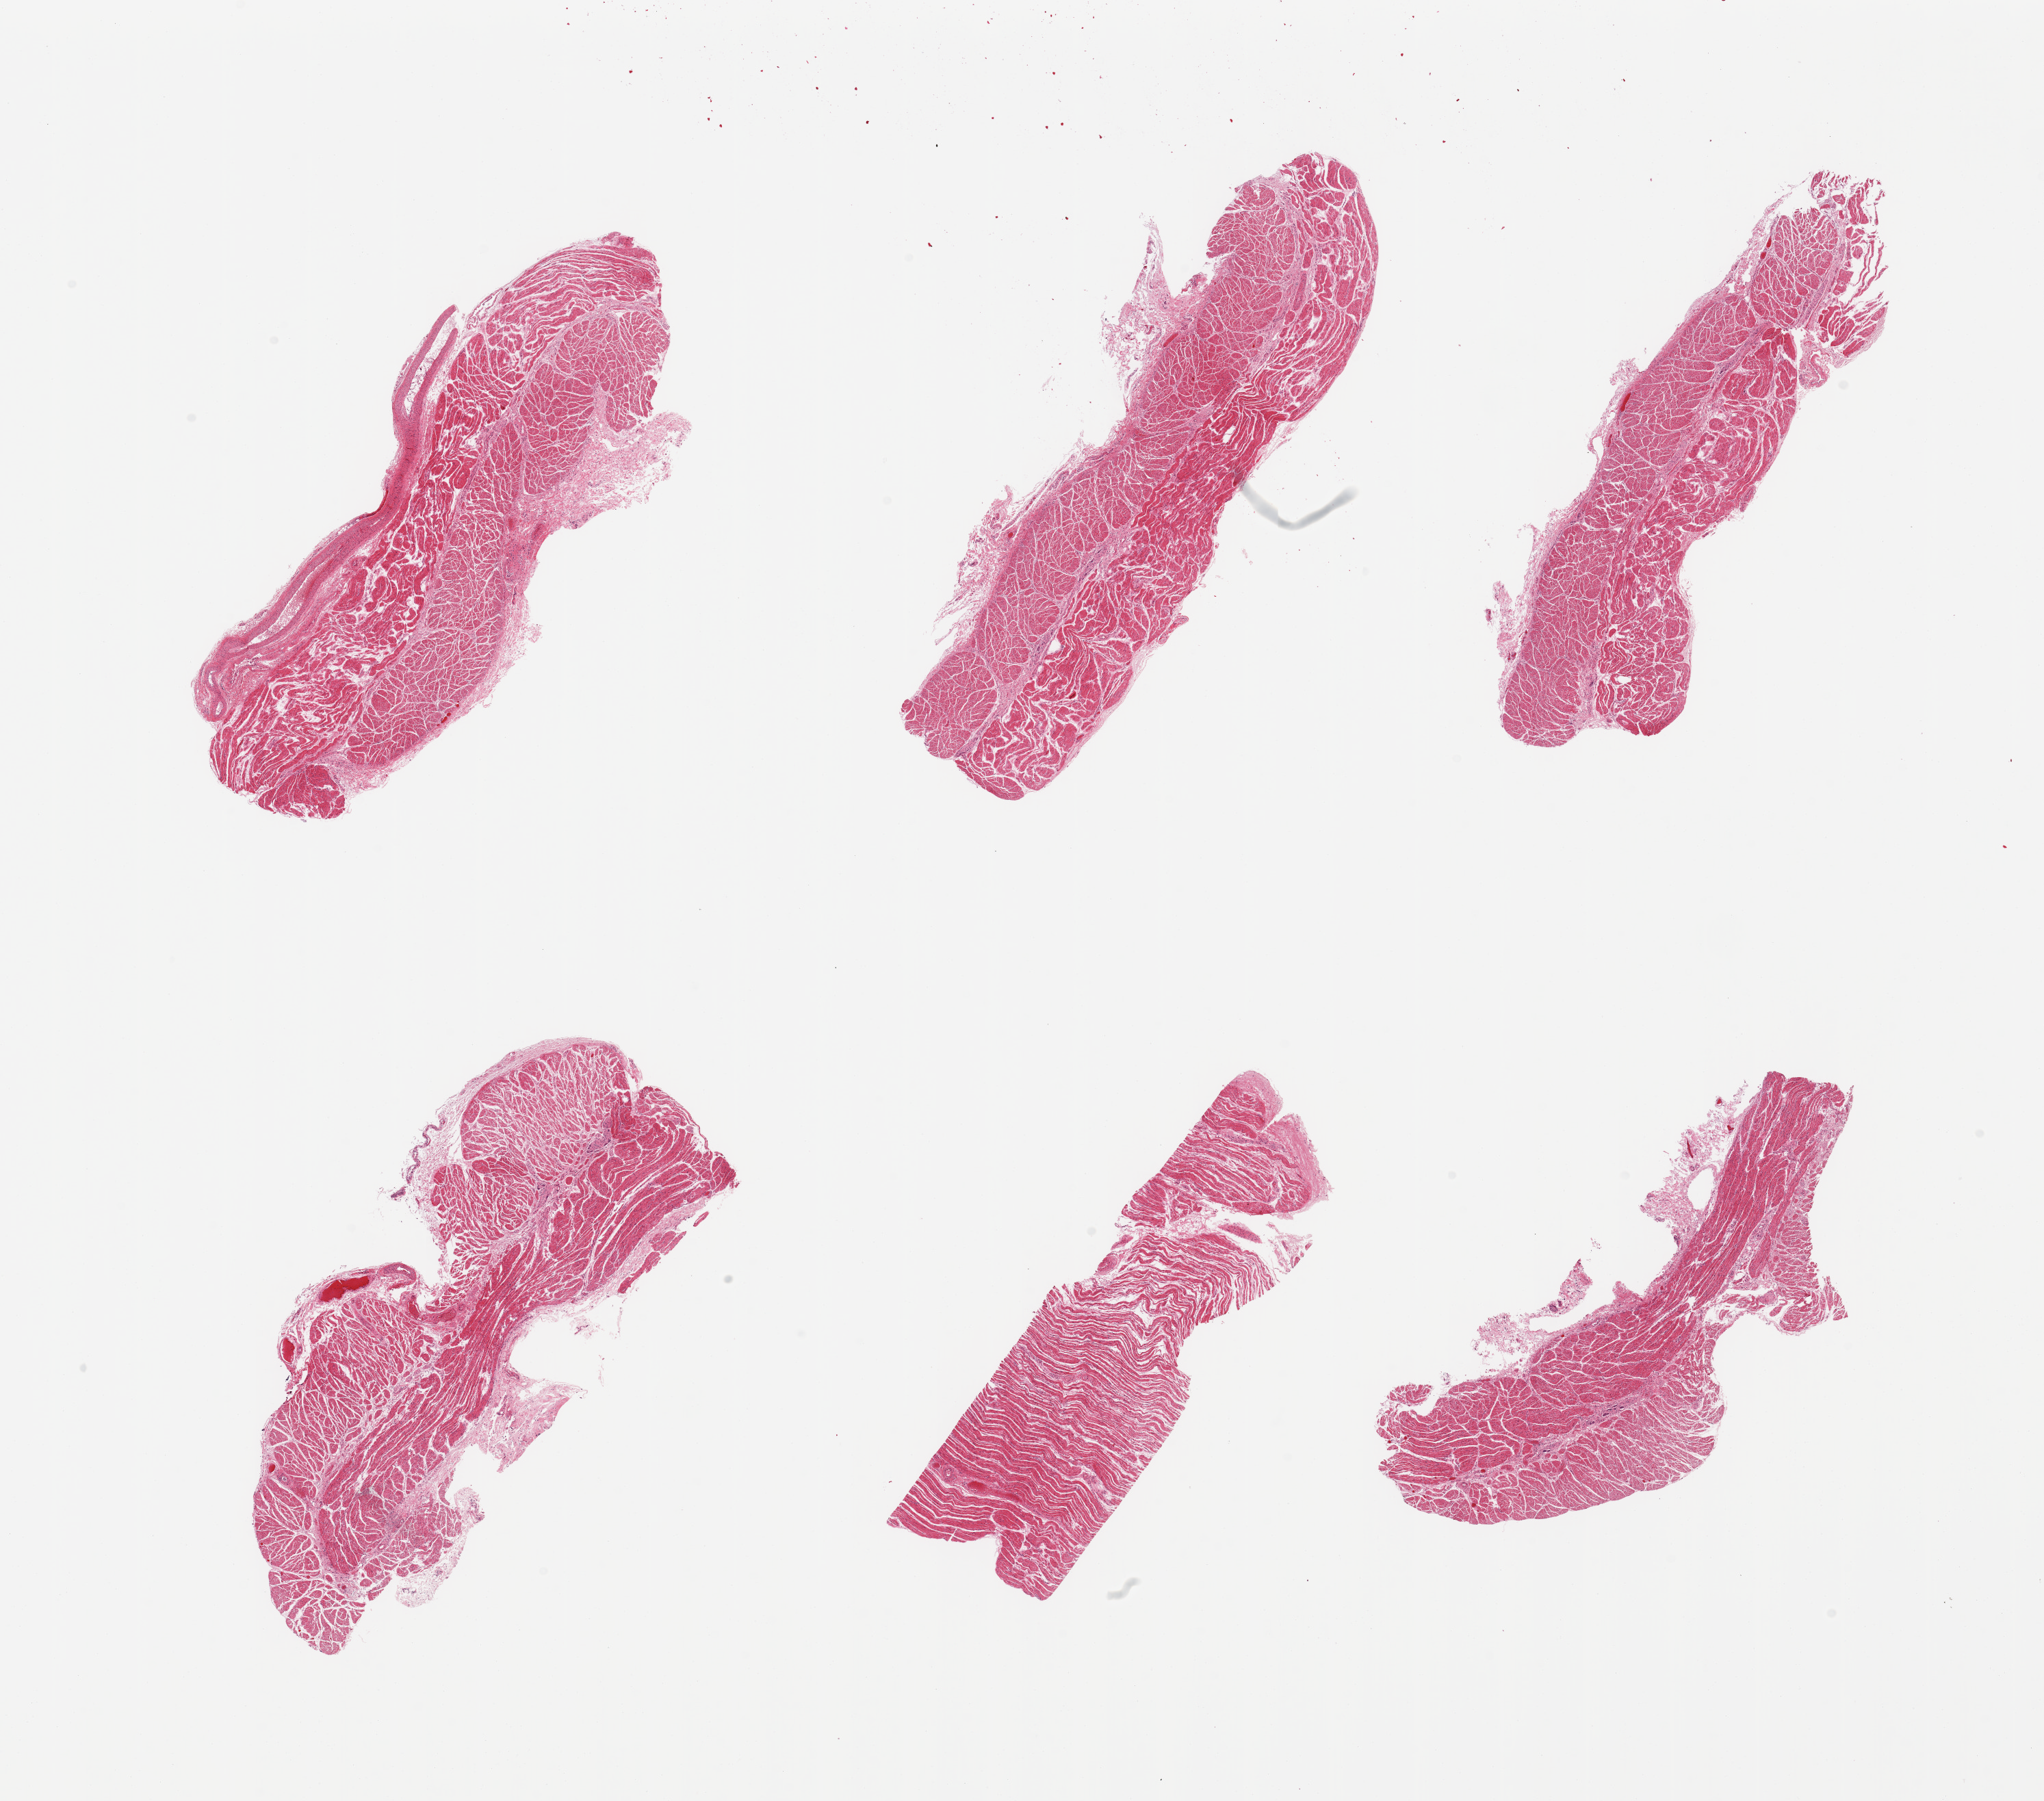
Digitized hematoxylin and eosin (H&E)-stained section — low-resolution overview of the scanned area, about 23.6 x 20.8 mm. PAXgene-fixed, paraffin-embedded tissue. Sampled site (target tissue): esophageal muscle. Donor tissue sample. Male donor.
• review note (as recorded): 6 pieces; well dissected; large adventitial artery in 1 piece